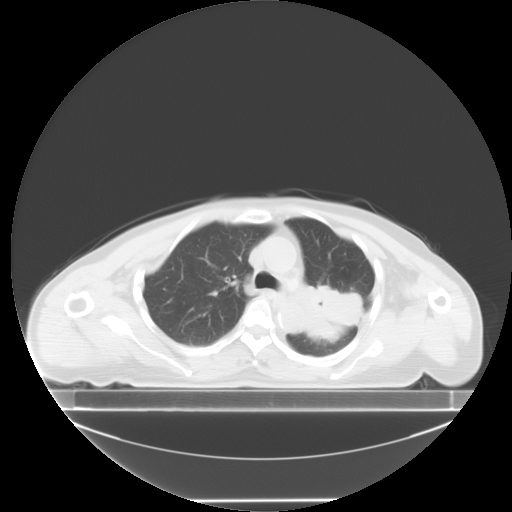
Chest CT, one axial slice. Position 7 of 24 along the scan axis. Reconstruction kernel STANDARD. 120 kVp. Lung window (W 1500 / L -600 HU). 5 mm slice thickness. 512 × 512 image matrix, field of view 500 × 500 mm. Patient: female, 74 years. From the clinical record (not read from this slice): clinical TNM (as recorded): T3 N1 M1c; histopathological grade: G3.
Outlined on this slice (rectangle marked by the reading radiologist):
- lung tumour (recorded histology: small cell carcinoma): bounding box (x1, y1, x2, y2) in pixels: (299, 277, 363, 350)